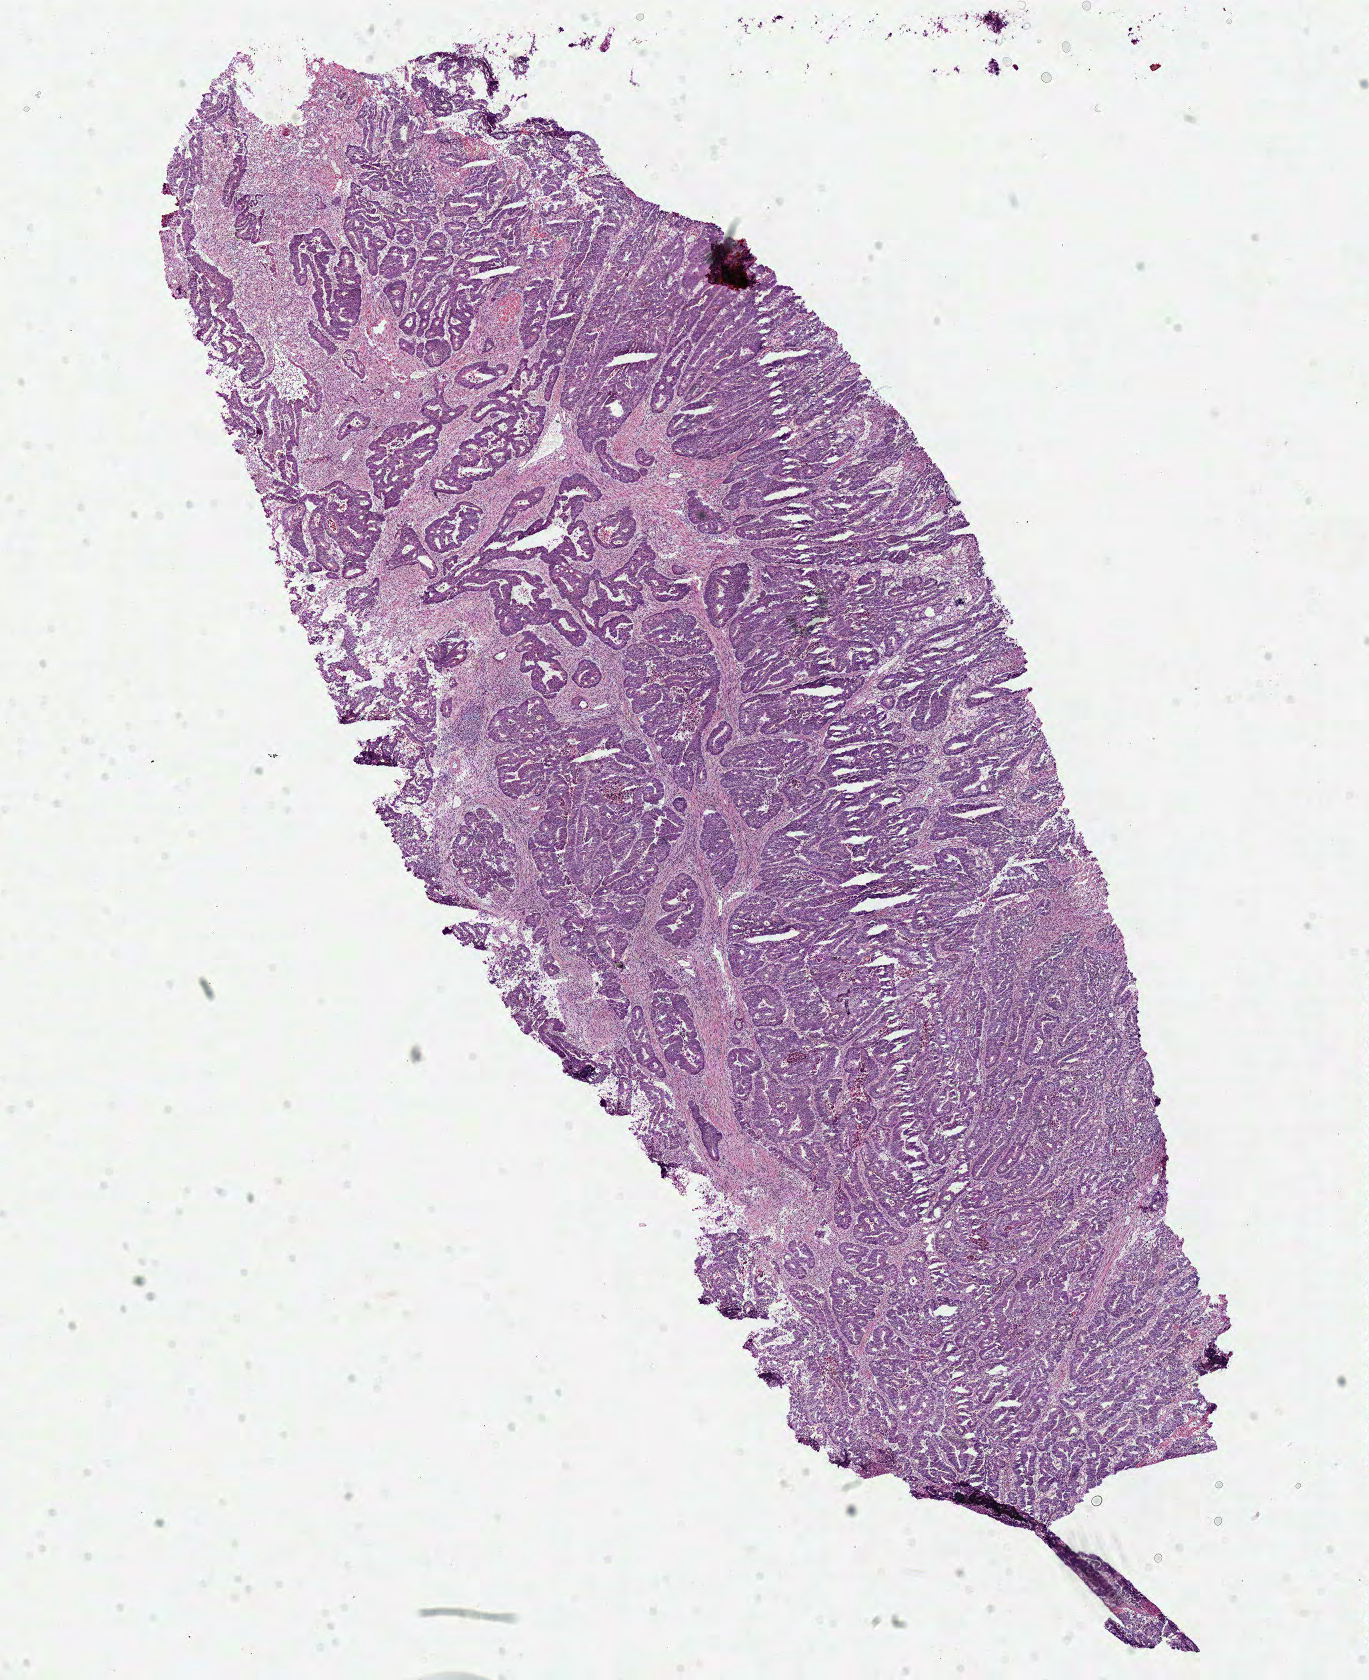
H&E-stained whole-slide image — whole scanned area (about 10.8 x 13.2 mm) shown as a low-resolution overview. Frozen section from the top of the tissue portion. Colon, primary tumour sample. Patient: male, age at initial diagnosis 66 years. Slide review estimates, as recorded: tumour cells 83%, tumour nuclei 80%, normal cells 0%, stromal cells 12%, necrosis 5%.
Diagnosis: Adenocarcinoma, NOS. Lymph nodes positive (case pathology): 1 of 82 examined. AJCC pathologic stage: IV.